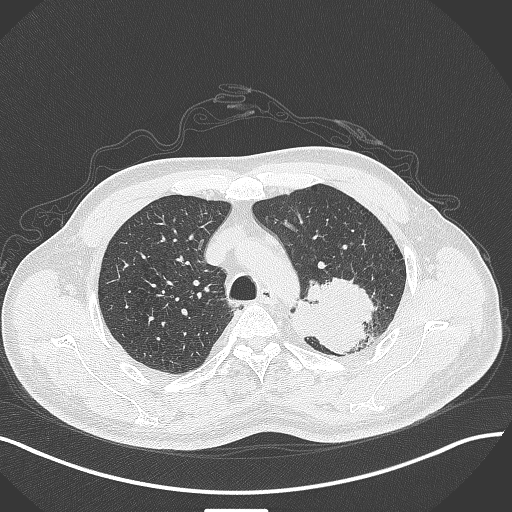
Chest CT, one axial slice. Slice 325 of 429 in the series (ordered by position). Reconstruction kernel B70f. 120 kVp. Lung window (W 1500 / L -600 HU). 1 mm slice thickness. 512 × 512 image matrix. Male patient, age 55 years. From the clinical record (not read from this slice): clinical TNM (as recorded): T3 N0 M1c.
Outlined on this slice (bounding box drawn by a radiologist):
- lung tumour (recorded histology: adenocarcinoma): bounding box (x1, y1, x2, y2) in pixels: (292, 277, 381, 361)